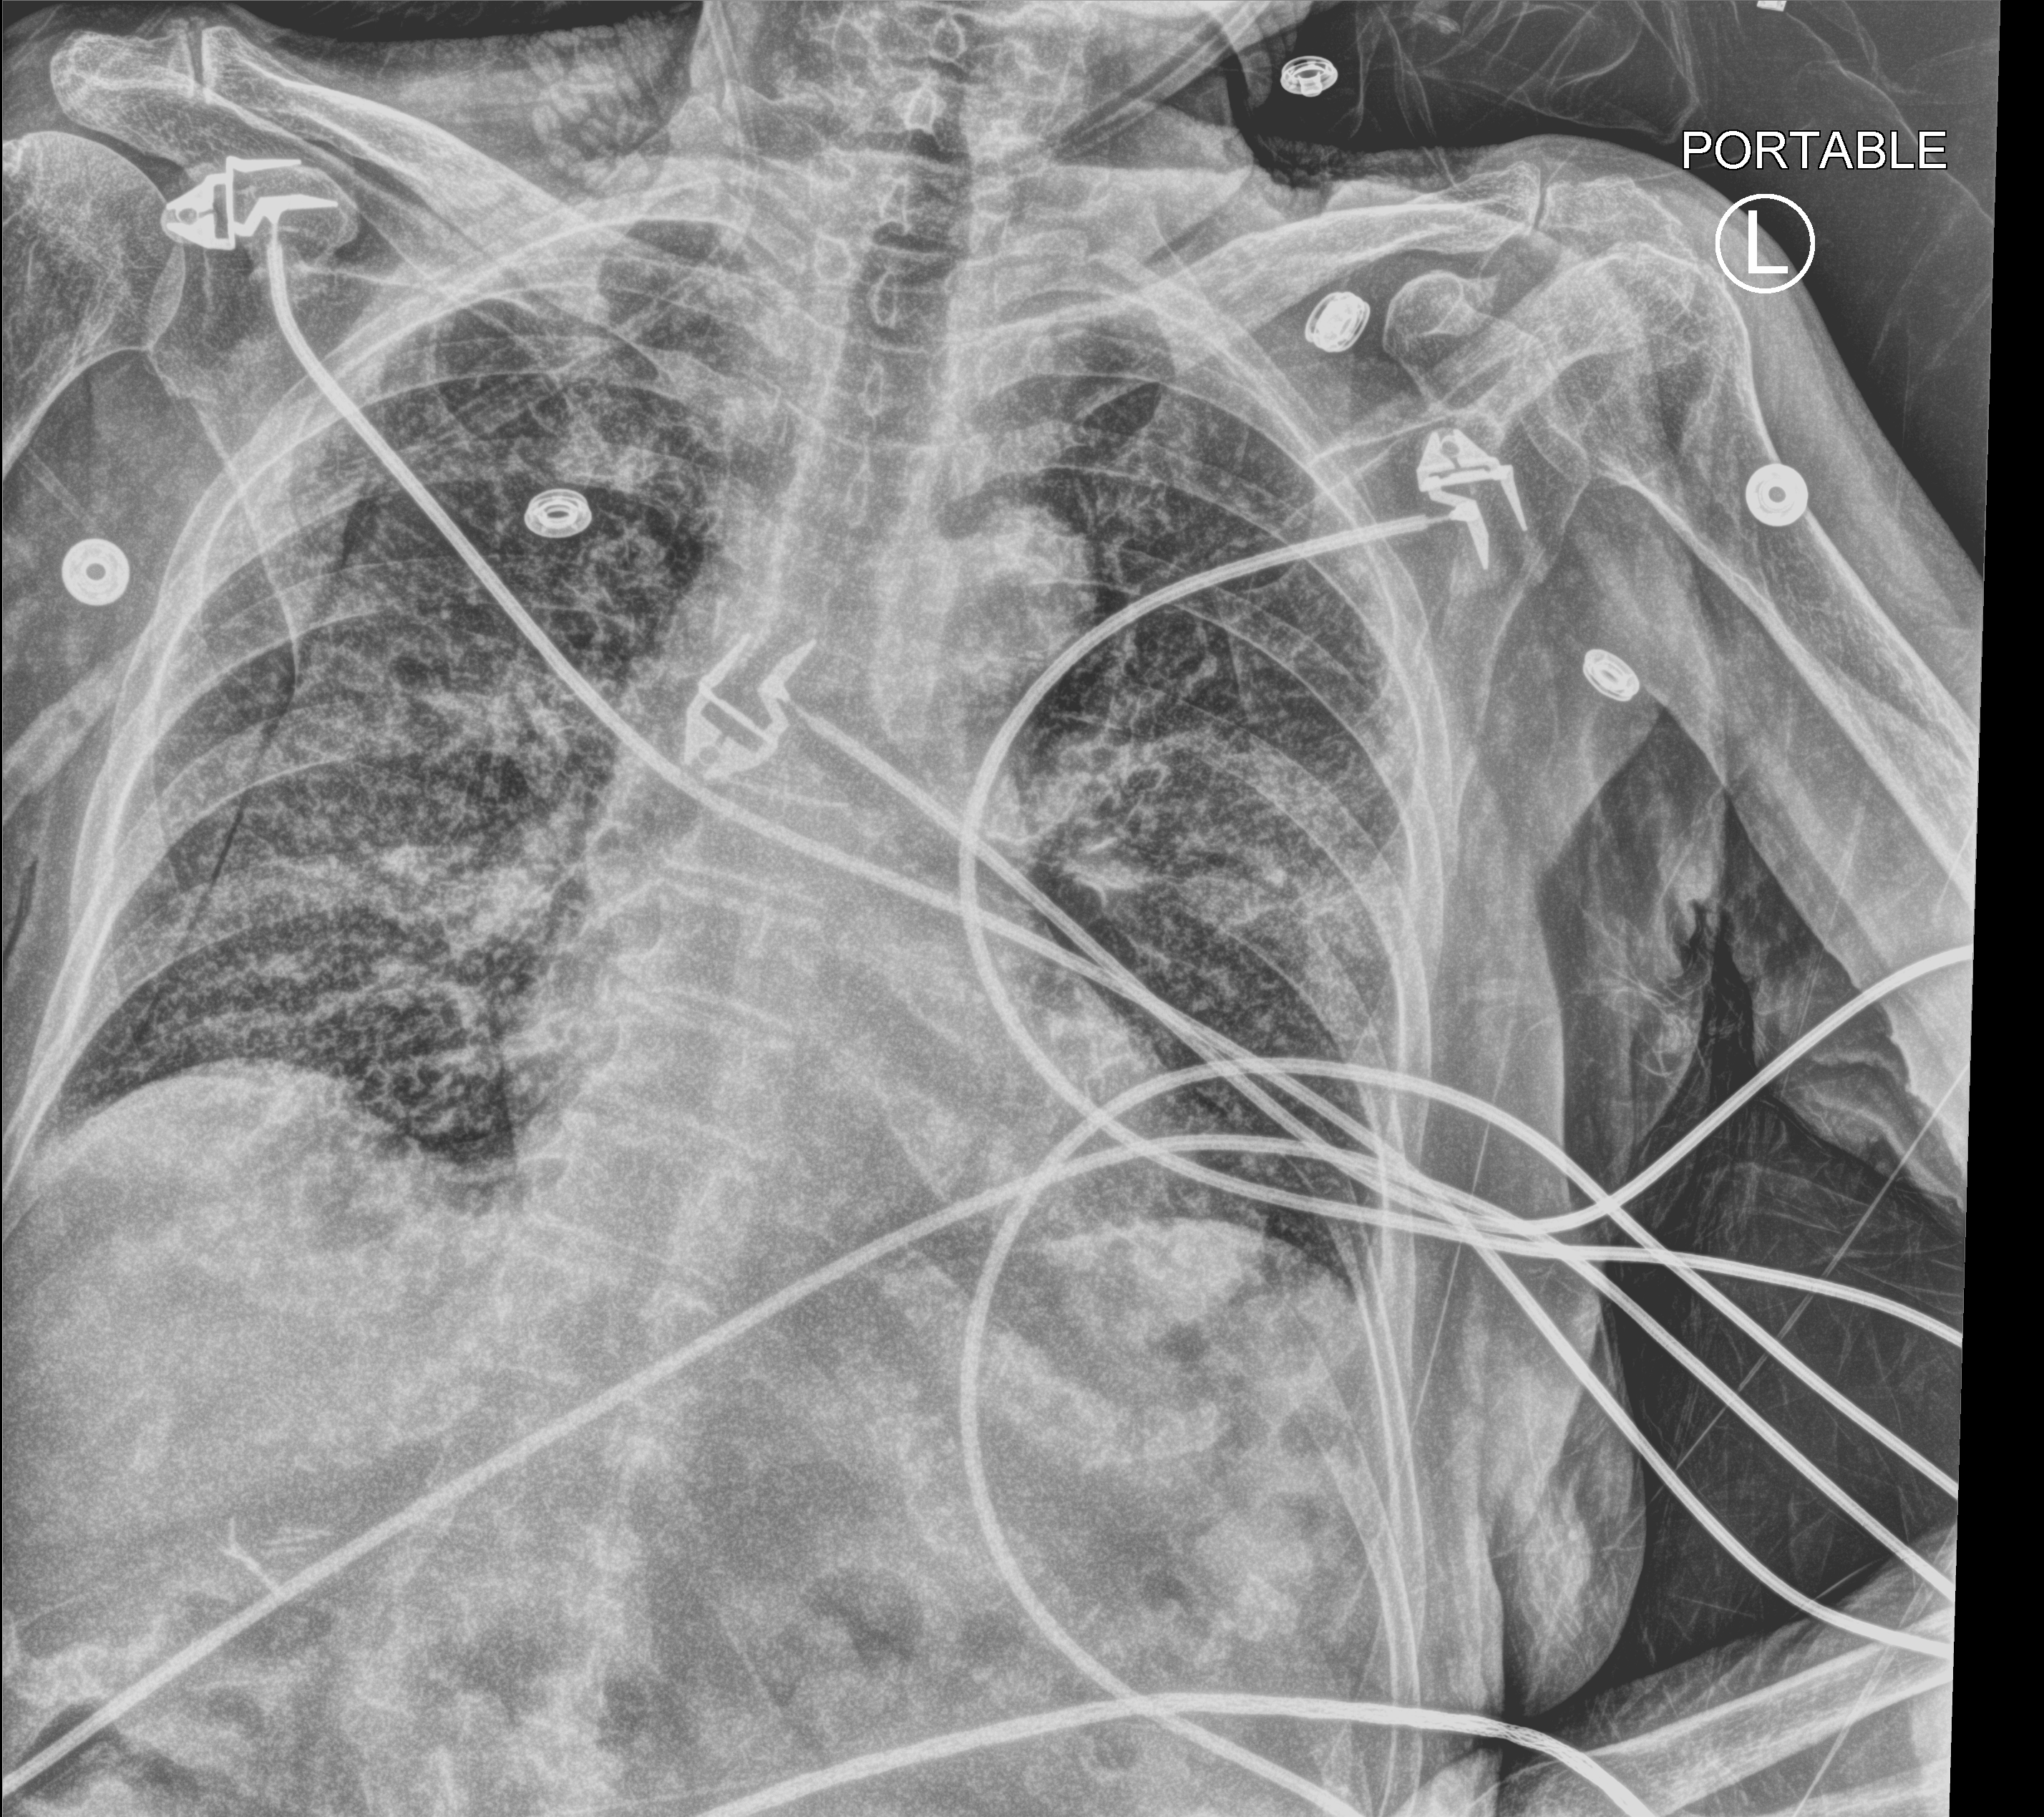
Chest X-ray (portable), anteroposterior (AP) projection. Patient hospitalised with COVID-19; female, aged 75–90 years.
Hospital-stay facts (about this admission, not read from this image; timing relative to this image not recorded):
- mechanically ventilated during this hospital stay: no
- admitted to intensive care during this hospital stay: no